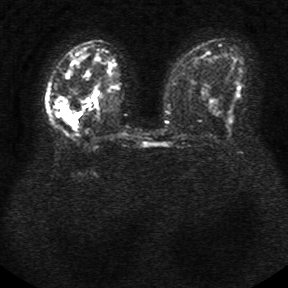
Breast MRI, one axial slice; position 15 of 34 along the scan axis; diffusion-weighted series; image 2 of 4 stored at this slice position (different b-values; order by instance number); 1.5 T; 5 mm slice thickness; 288 × 288 image matrix, field of view 340 × 340 mm. Female patient.
Structures marked on this image (outlined manually by an expert reader):
- tumour on diffusion-weighted imaging: box from (x=76, y=89) to (x=100, y=118) px